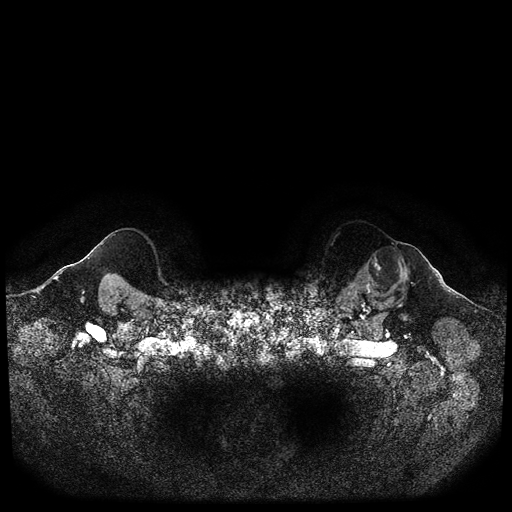
Breast MRI (dynamic contrast-enhanced, multi-phase), one axial slice. Dynamic contrast-enhanced series, time point 2 of 5 at this slice position (early post-contrast). 1.5 T. TE 2.6 ms, TR 5.3 ms. 2 mm slice thickness. 512 × 512 image matrix. Female patient, age 64 years.
Annotated regions visible in this slice (semi-automatically segmented with operator editing):
- breast lesion (labelled 'tumour' in the annotation; benign lesions carry a separate 'benign' label): box from (x=361, y=246) to (x=410, y=299) px